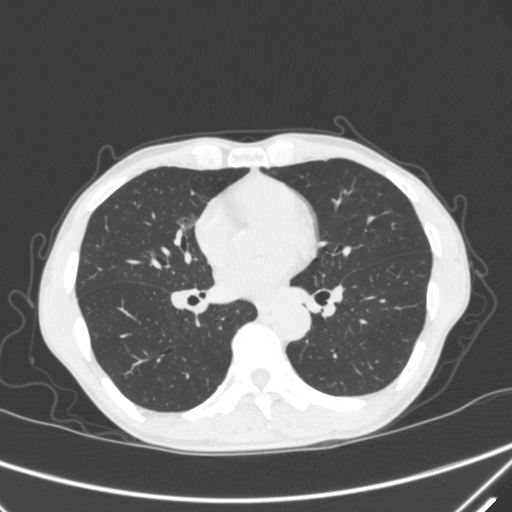
Chest CT, one axial slice. Slice 161 of 340 in the series (ordered by position). Lung window (W 1500 / L -600 HU). 512 × 512 image matrix, field of view 350 × 350 mm. Male patient, age 67 years. From the clinical record (not read from this slice): clinical TNM (as recorded): T1c N0 M0; histopathological grade: G1-2.
Structures marked on this image (rectangle marked by the reading radiologist):
- lung tumour (recorded histology: adenocarcinoma): bounding box (x1, y1, x2, y2) in pixels: (174, 207, 201, 242)